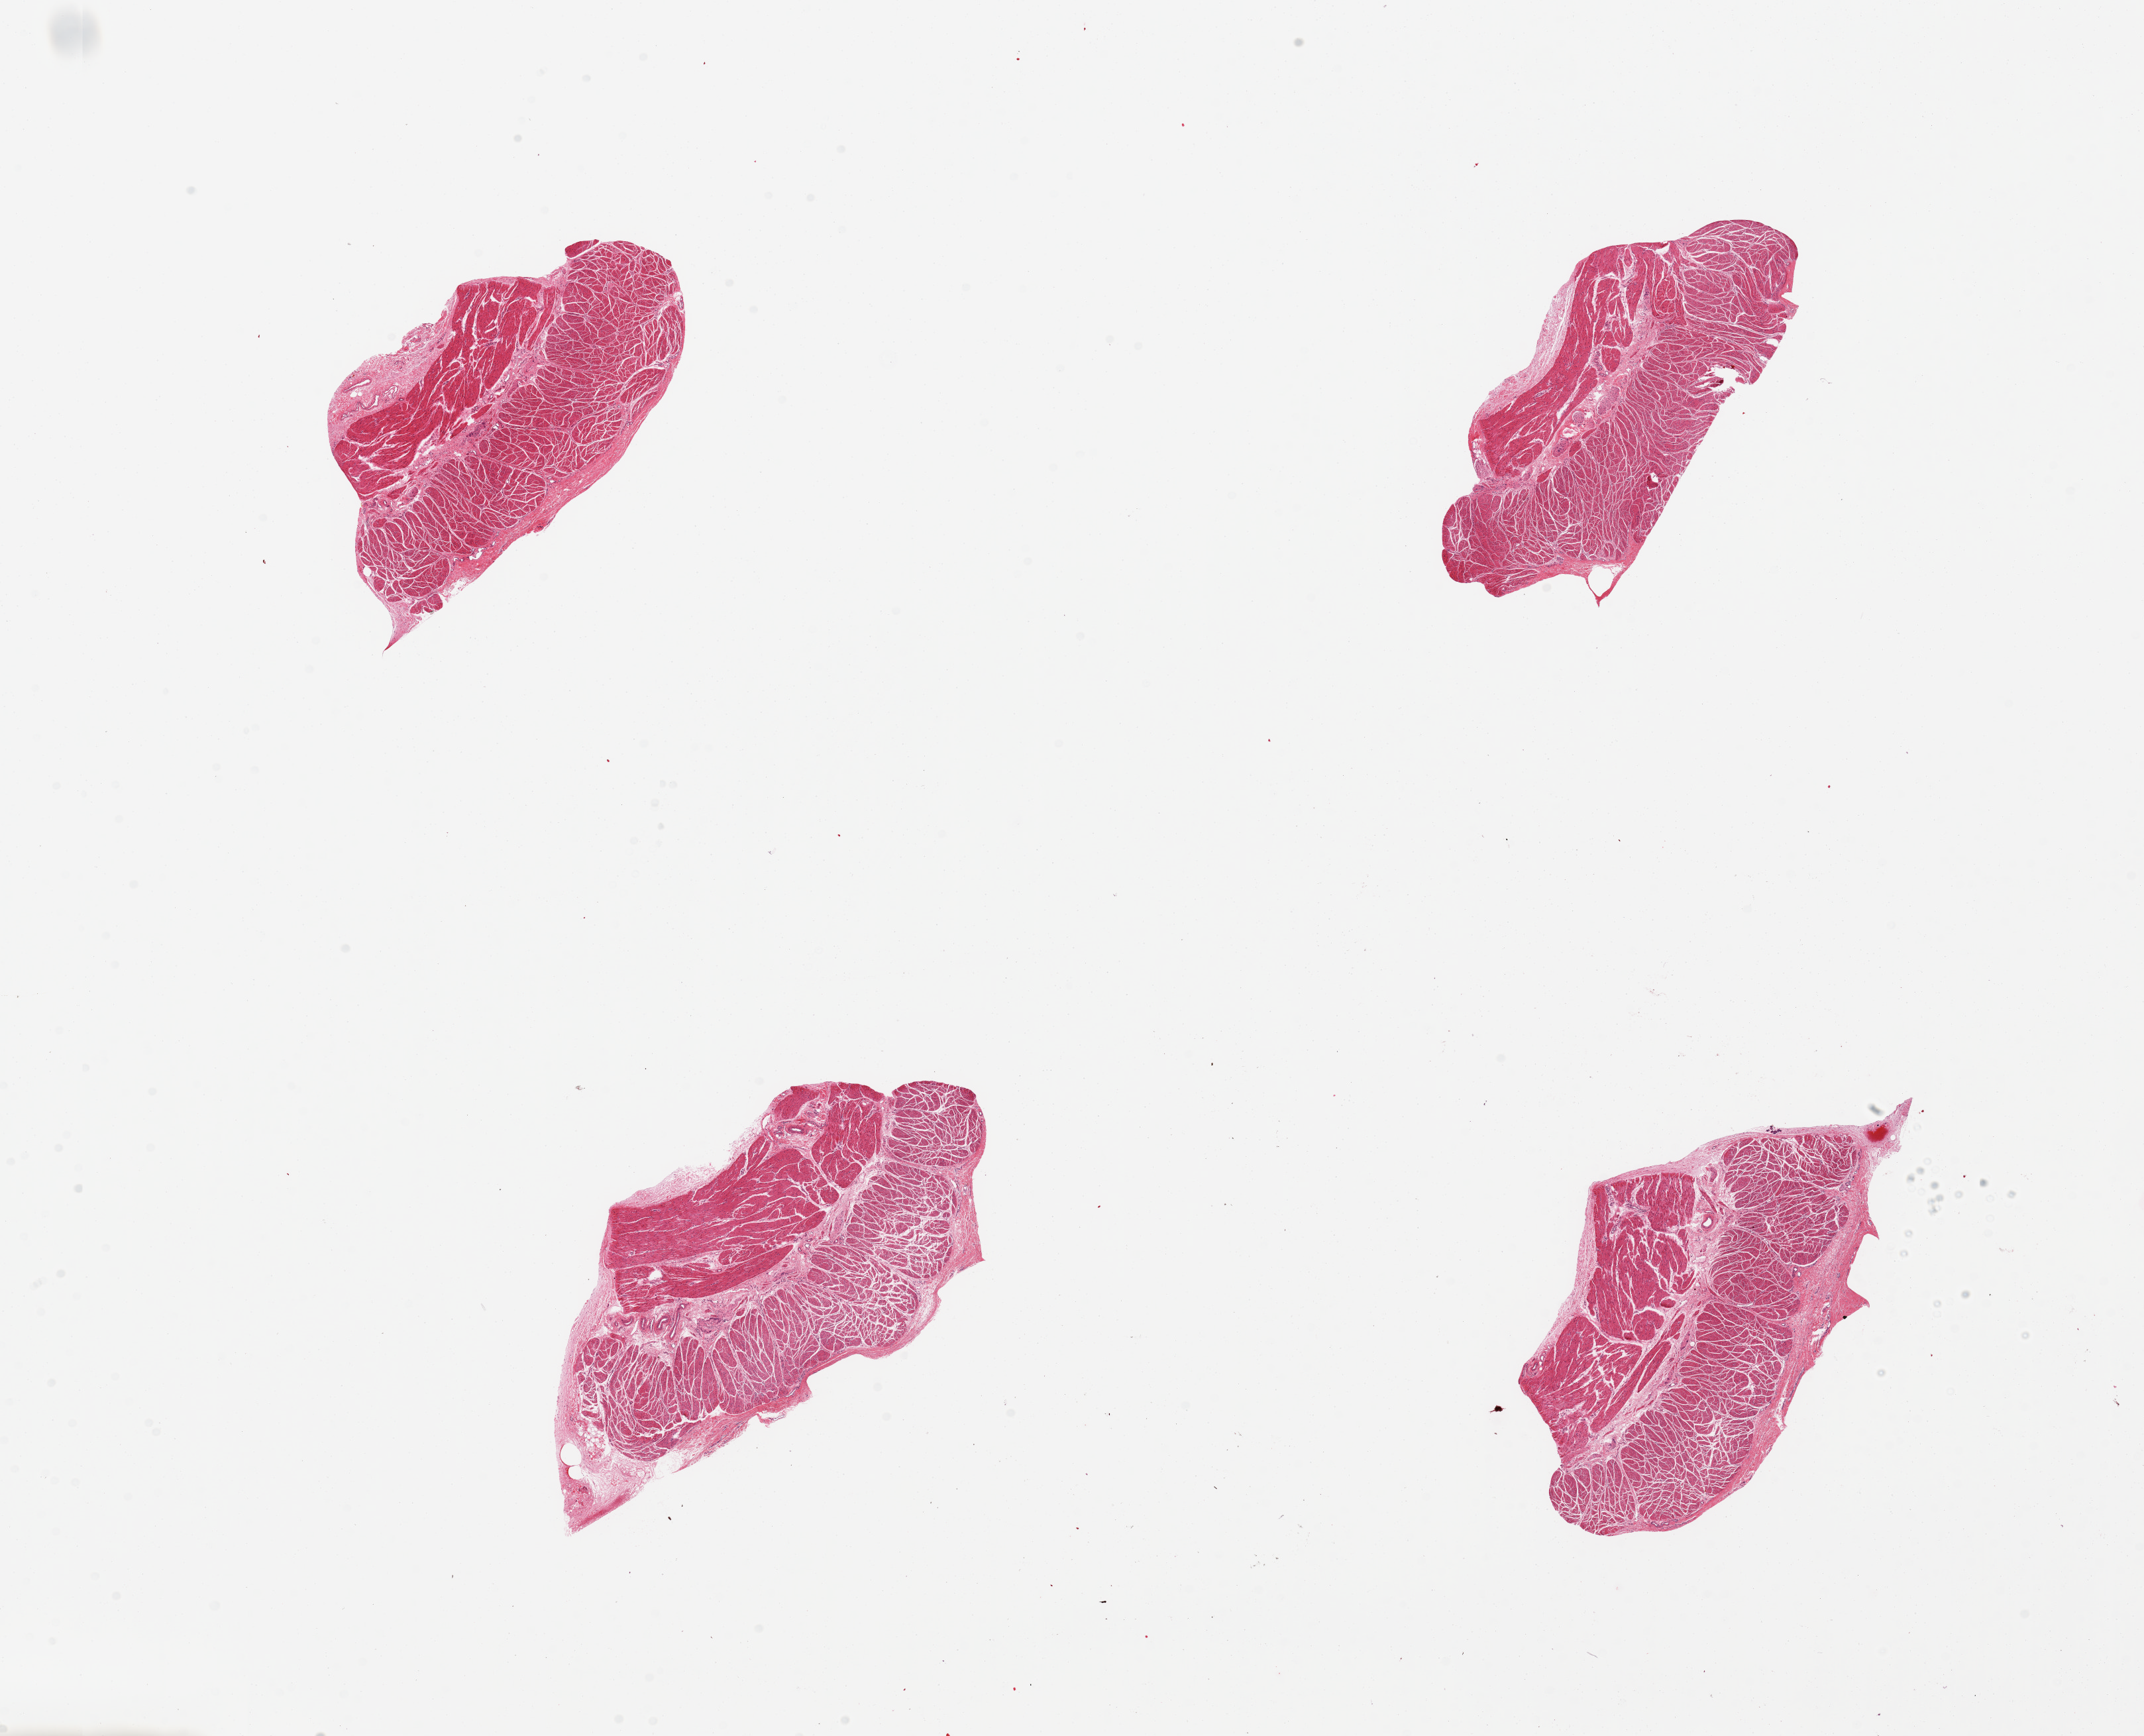
Whole-slide image, hematoxylin and eosin (H&E) stain — whole scanned area (about 25.6 x 20.7 mm) shown as a low-resolution overview, PAXgene-fixed paraffin-embedded (PFPE) section, target tissue: esophageal muscle, tissue donor sample. Donor sex: male.
Pathologist's review note for this sample: 4 pieces; muscularis, not mucosa.